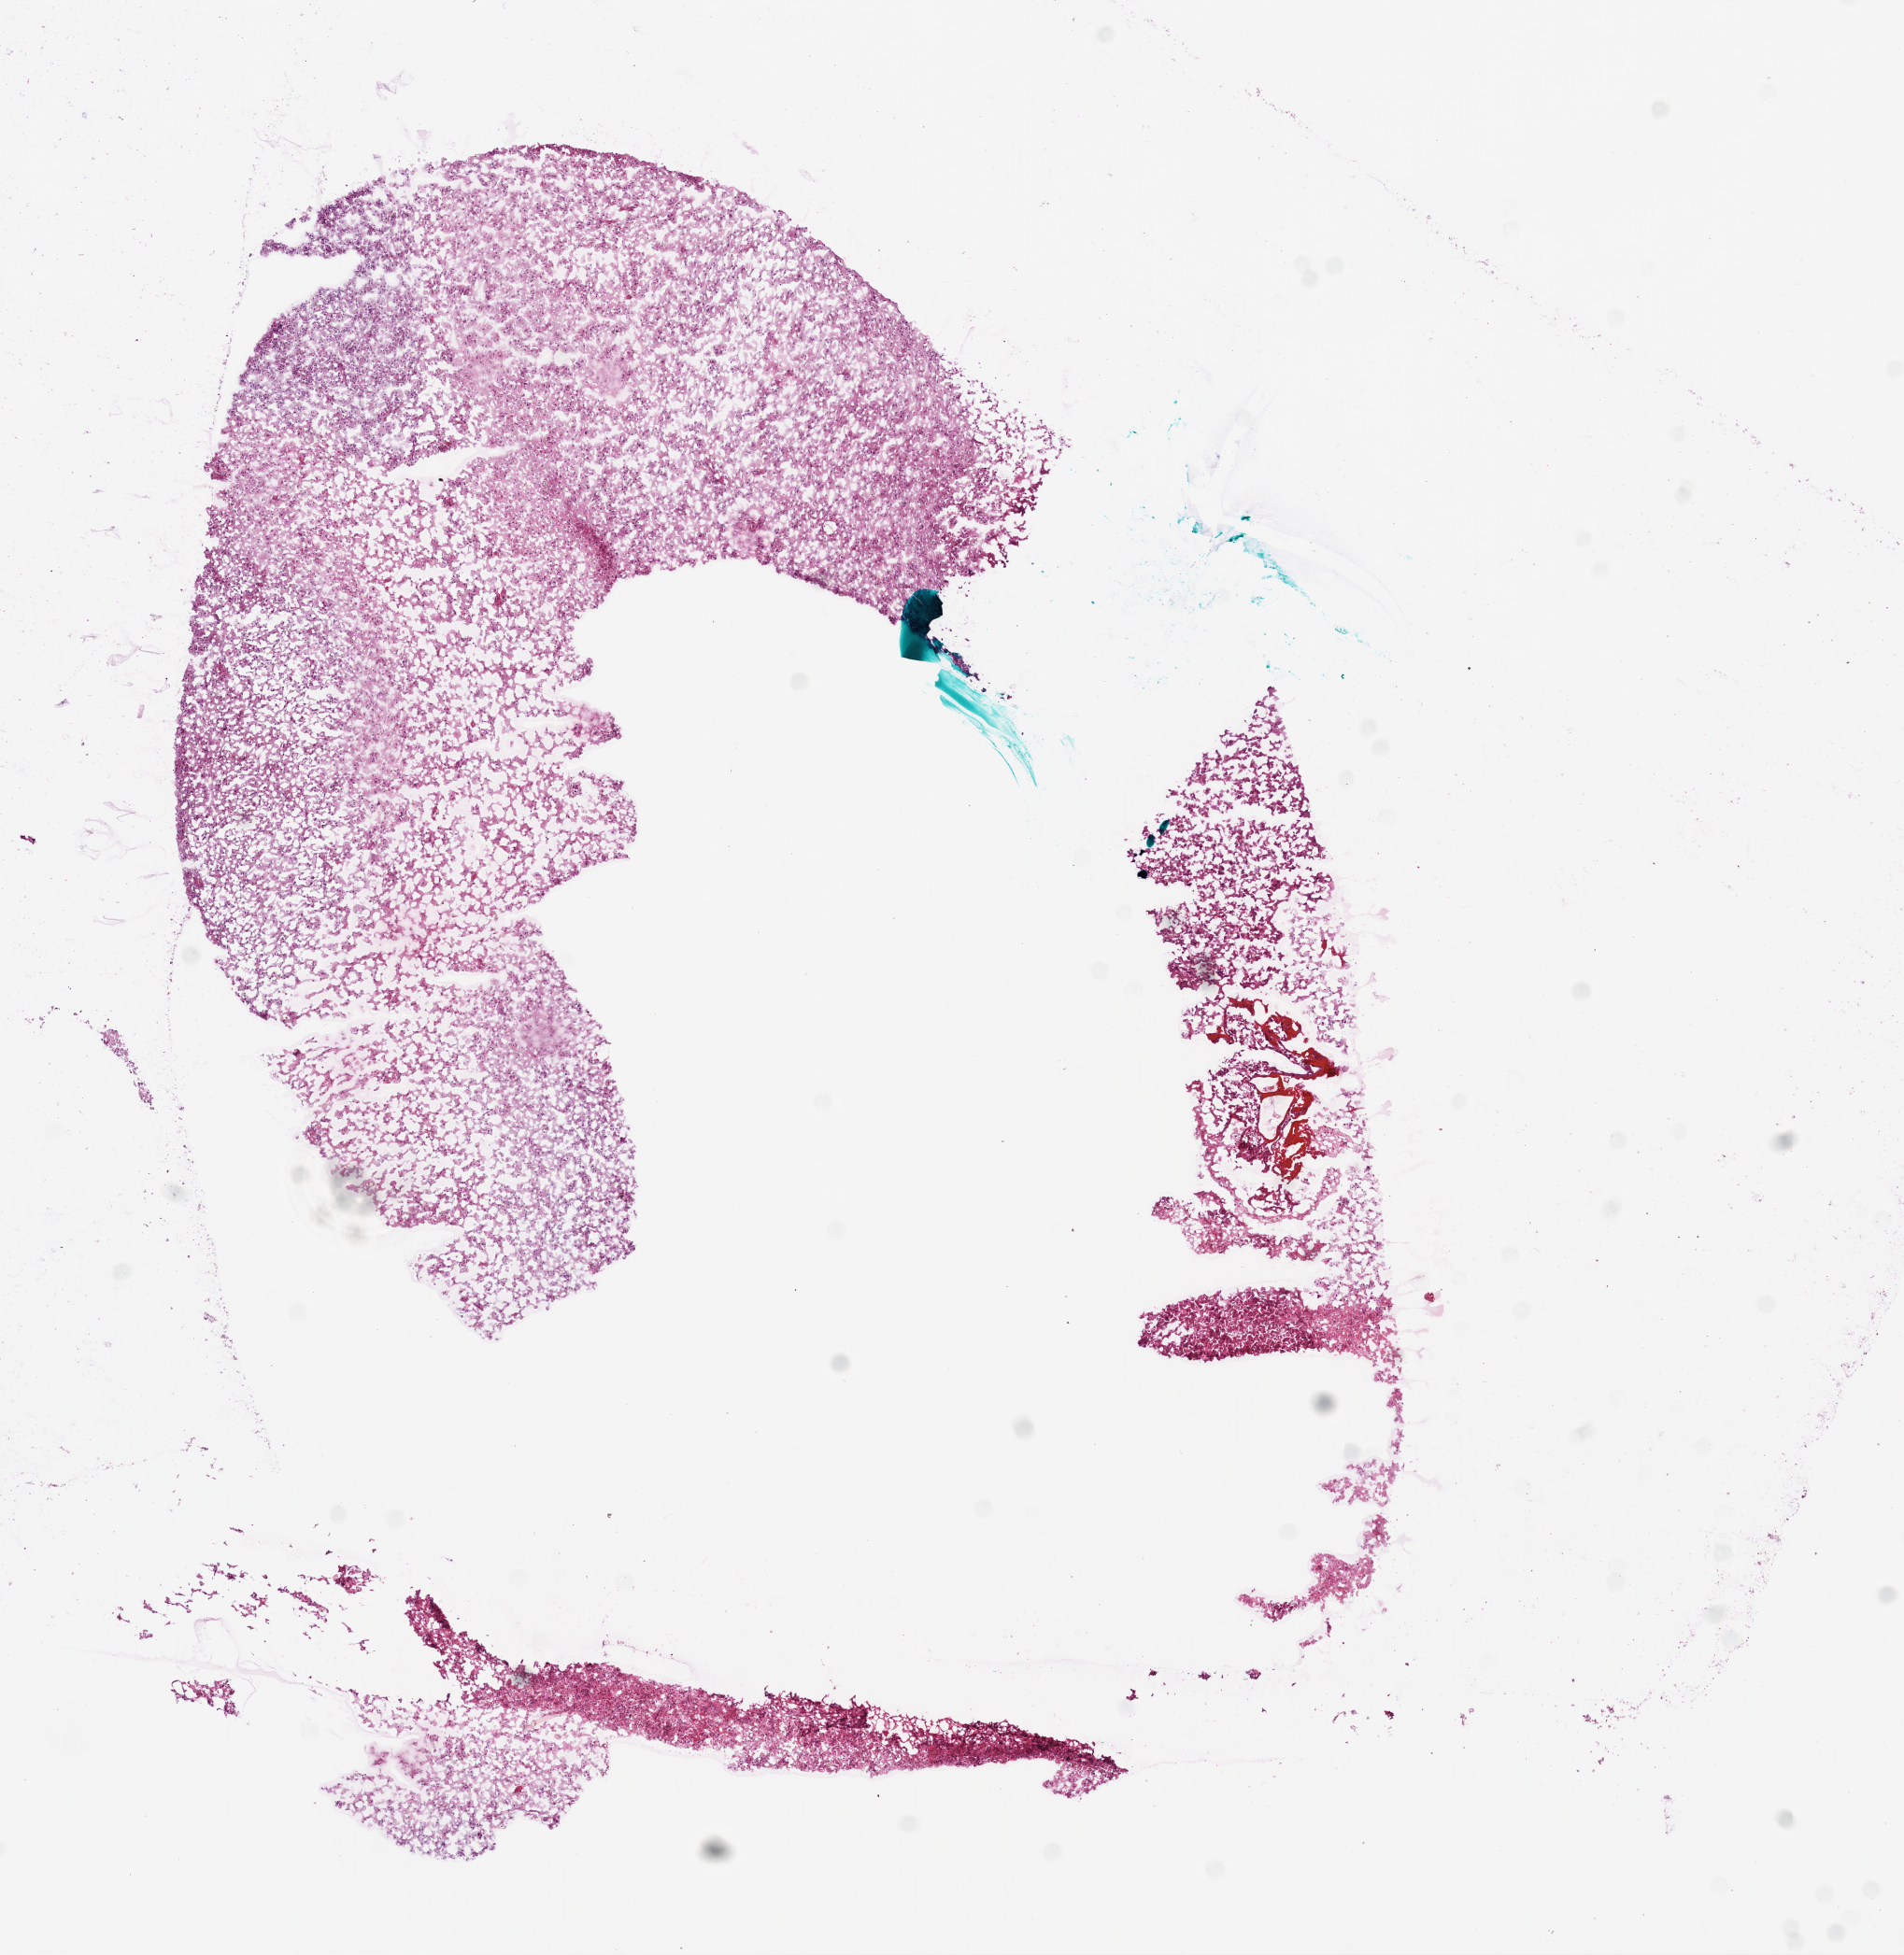
Whole-slide histology image, H&E — whole scanned area (about 8.2 x 8.4 mm, slide scanned at 20x) shown as a low-resolution overview; frozen section from the bottom of the tissue portion; sample: primary tumour, brain. Patient: female, age at initial diagnosis 48 years.
Diagnosis: Glioblastoma.